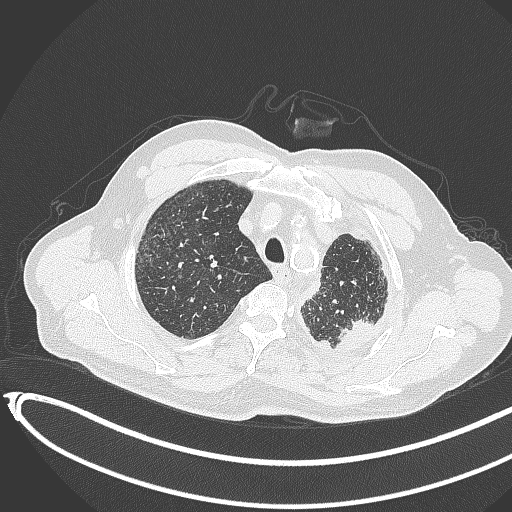
Chest CT, one axial slice. Slice 357 of 451 in the series (ordered by position). 120 kVp. Lung window (W 1500 / L -600 HU). 1 mm slice thickness. 512 × 512 image matrix. Male patient, age 78 years. From the clinical record (not read from this slice): clinical TNM (as recorded): T1c N0 M1.
Structures marked on this image (bounding box drawn by a radiologist):
- lung tumour (recorded histology: adenocarcinoma): bounding box [x1, y1, x2, y2] px = [336, 314, 378, 354]